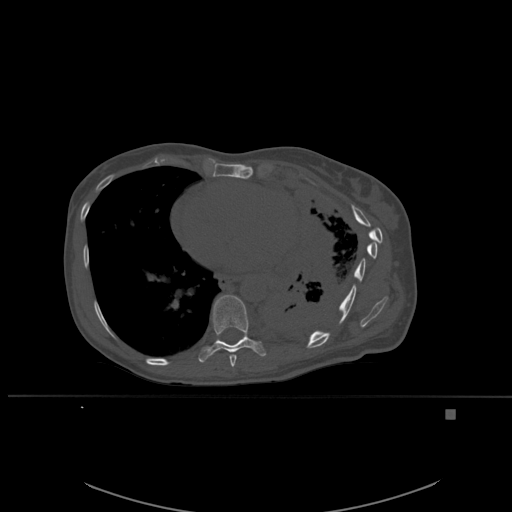
CT including the spine, one axial slice; slice 335 of 537 in the series (ordered by position); bone window (W 1800 / L 400 HU); 1.5 mm slice thickness; 512 × 512 image matrix, field of view 440 × 440 mm. Female patient, age 45 years. Case-level facts recorded for this patient, not image findings: primary cancer: lung.
Annotated regions visible in this slice (semi-automatic segmentation, software-assisted and operator-edited):
- T8 vertebra: box from (x=229, y=353) to (x=237, y=367) px
- T9 vertebra: (x=198, y=295)–(x=266, y=363)